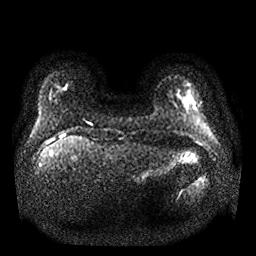
Breast MRI, one axial slice; diffusion-weighted series; image 2 of 4 stored at this slice position (different b-values; order by instance number); 1.5 T; 256 × 256 image matrix. Female patient.
Structures marked on this image (expert manual segmentation):
- tumour on diffusion-weighted imaging: bounding box [x1, y1, x2, y2] px = [184, 98, 192, 109]